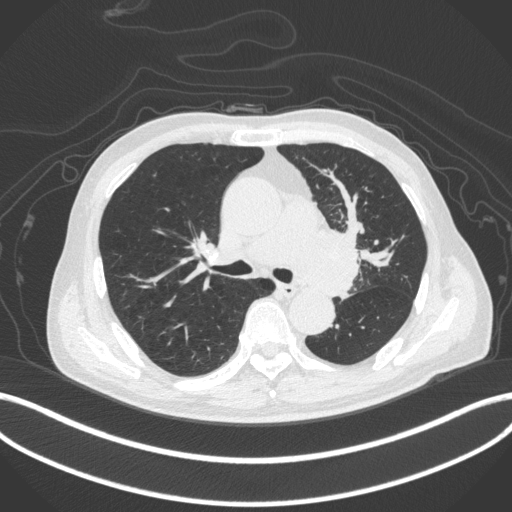
Chest CT, one axial slice; slice 270 of 420 in the series (ordered by position); reconstruction kernel B31f; 120 kVp; lung window (W 1500 / L -600 HU); 1 mm slice thickness; 512 × 512 image matrix, field of view 400 × 400 mm. Male patient, age 77 years. From the clinical record (not read from this slice): clinical TNM (as recorded): T3 N1 M0.
Structures marked on this image (bounding box drawn by a radiologist):
- lung tumour (recorded histology: adenocarcinoma): bounding box (x1, y1, x2, y2) in pixels: (292, 220, 364, 296)